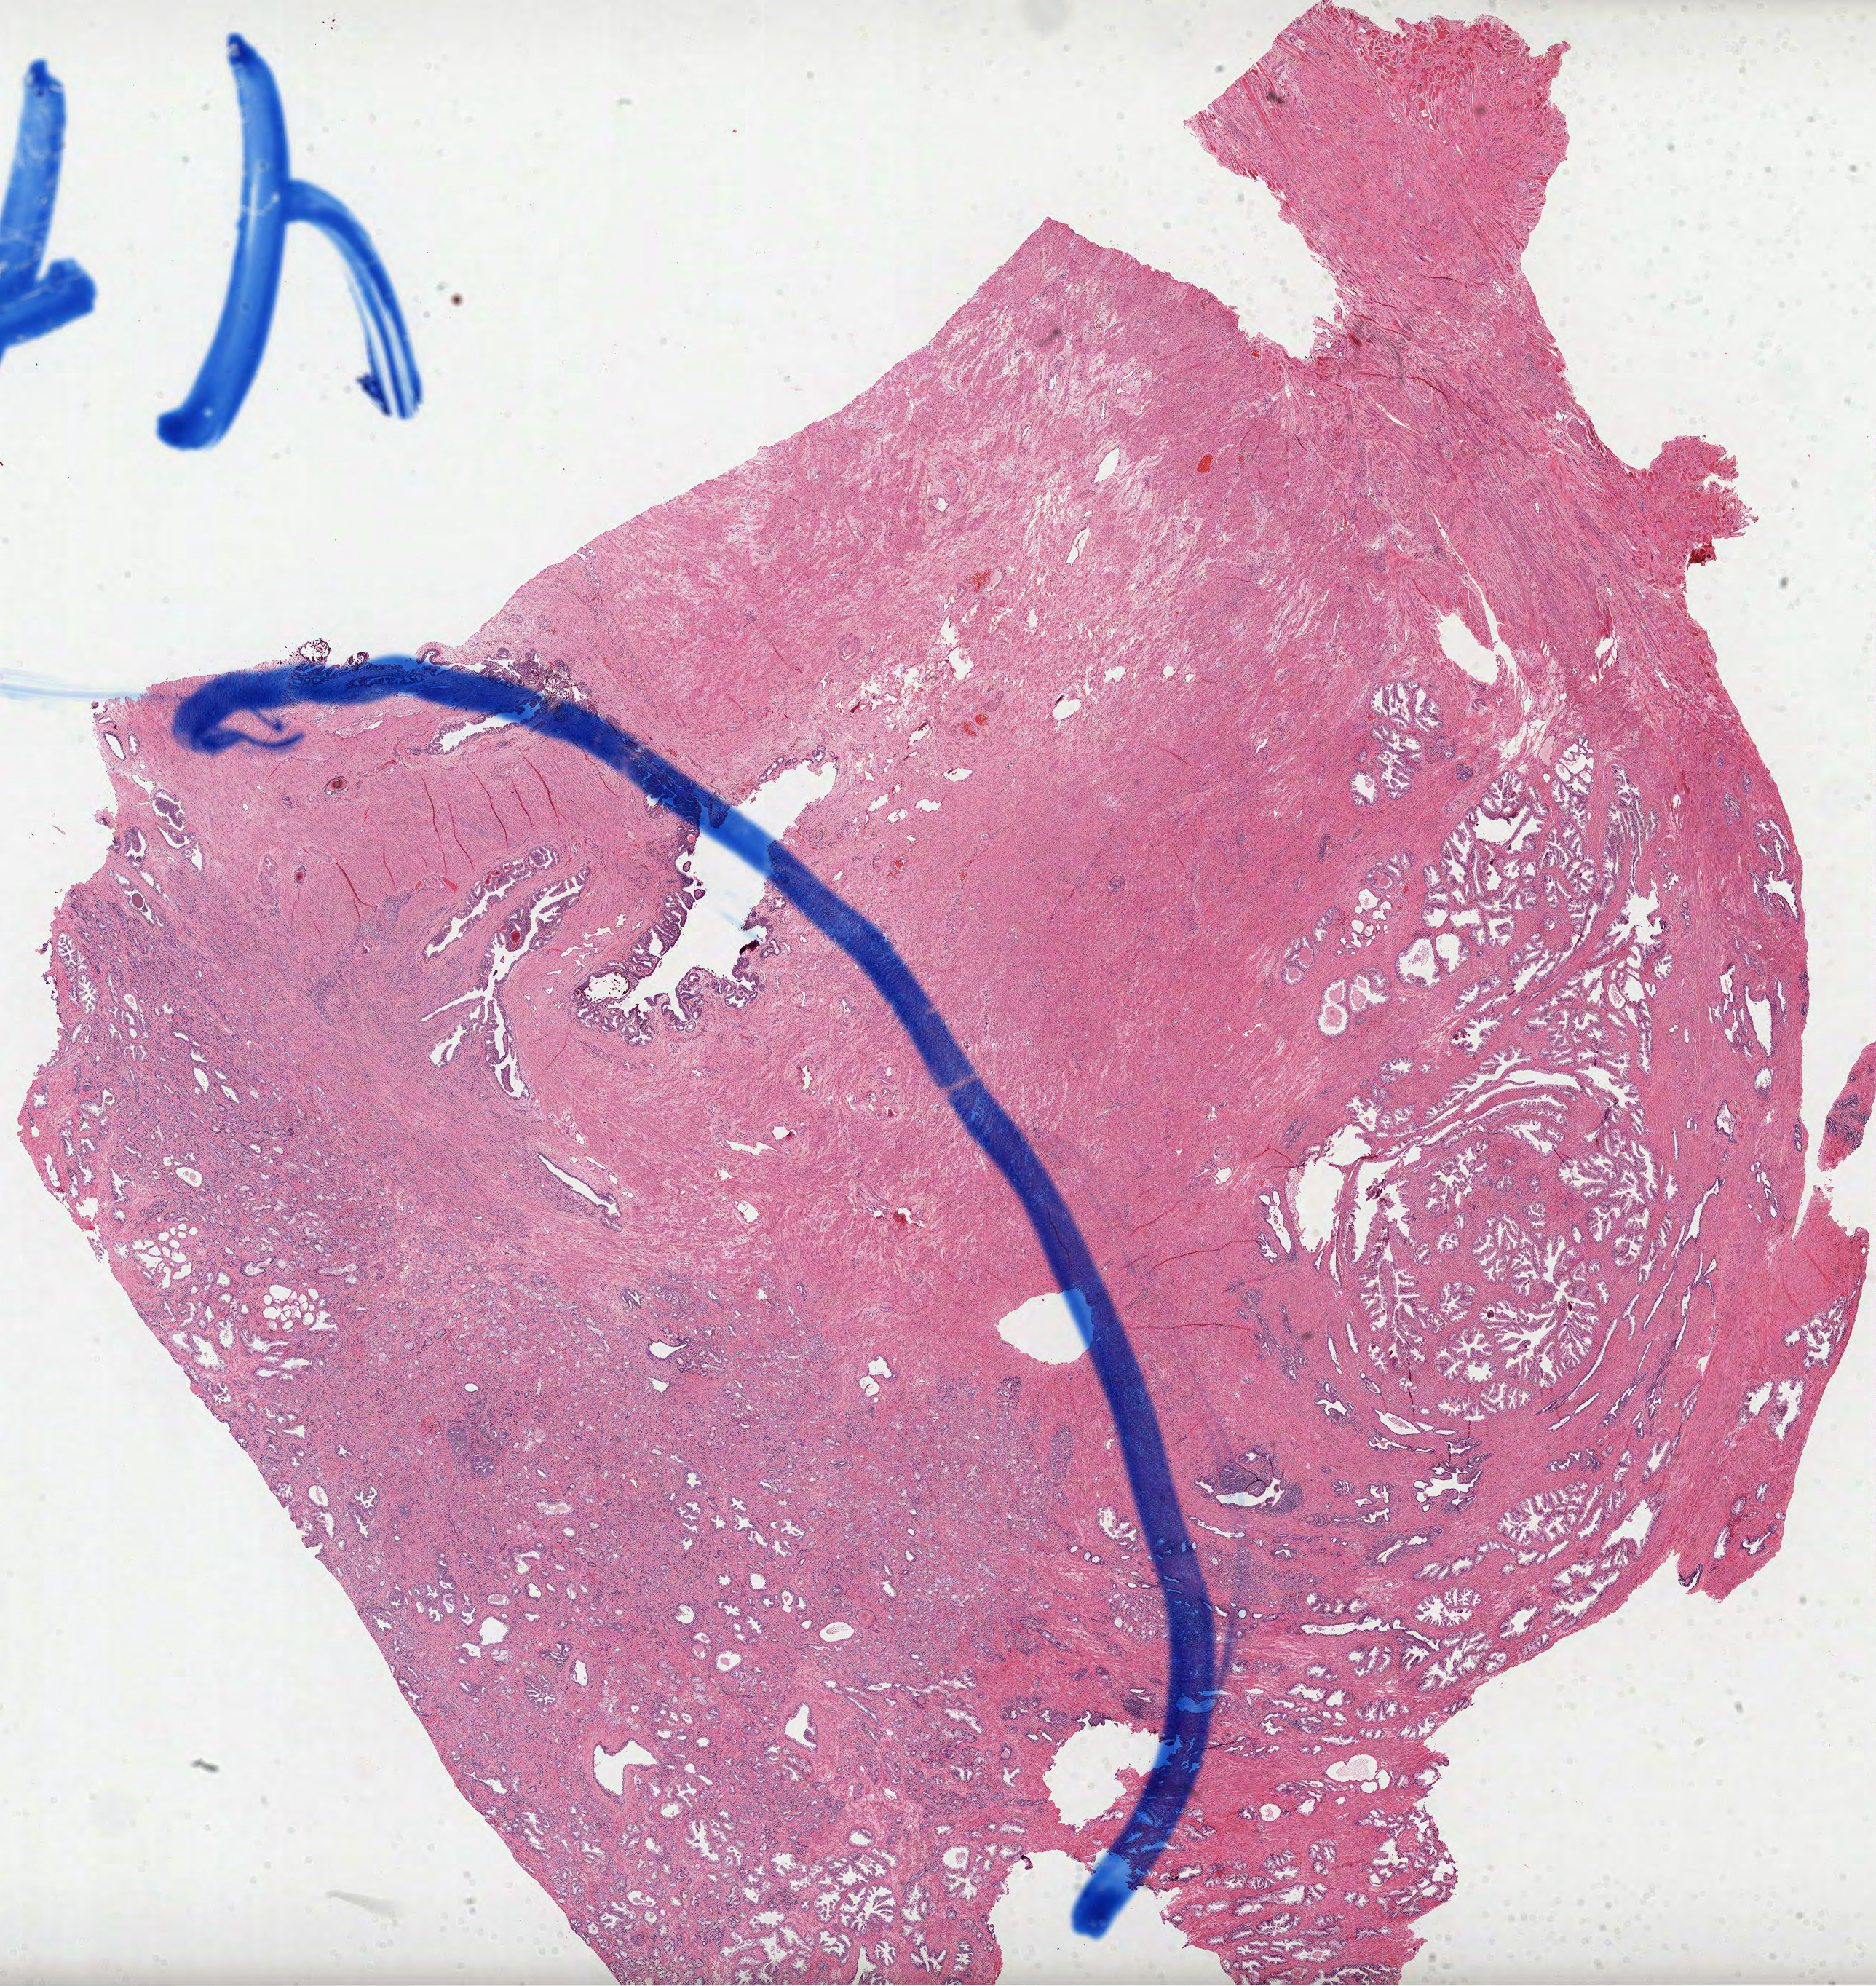
H&E-stained whole-slide image — shown as a low-resolution overview of the whole scanned area (about 20.8 x 22.0 mm); formalin-fixed paraffin-embedded (FFPE) diagnostic section; sample: primary tumour, prostate. Male patient; age at initial diagnosis 56 years. Gleason score: 7 (4+3).
* pathologic diagnosis: Acinar cell carcinoma (prostate gland)
* lymph nodes positive (case pathology): 0 of 26 examined